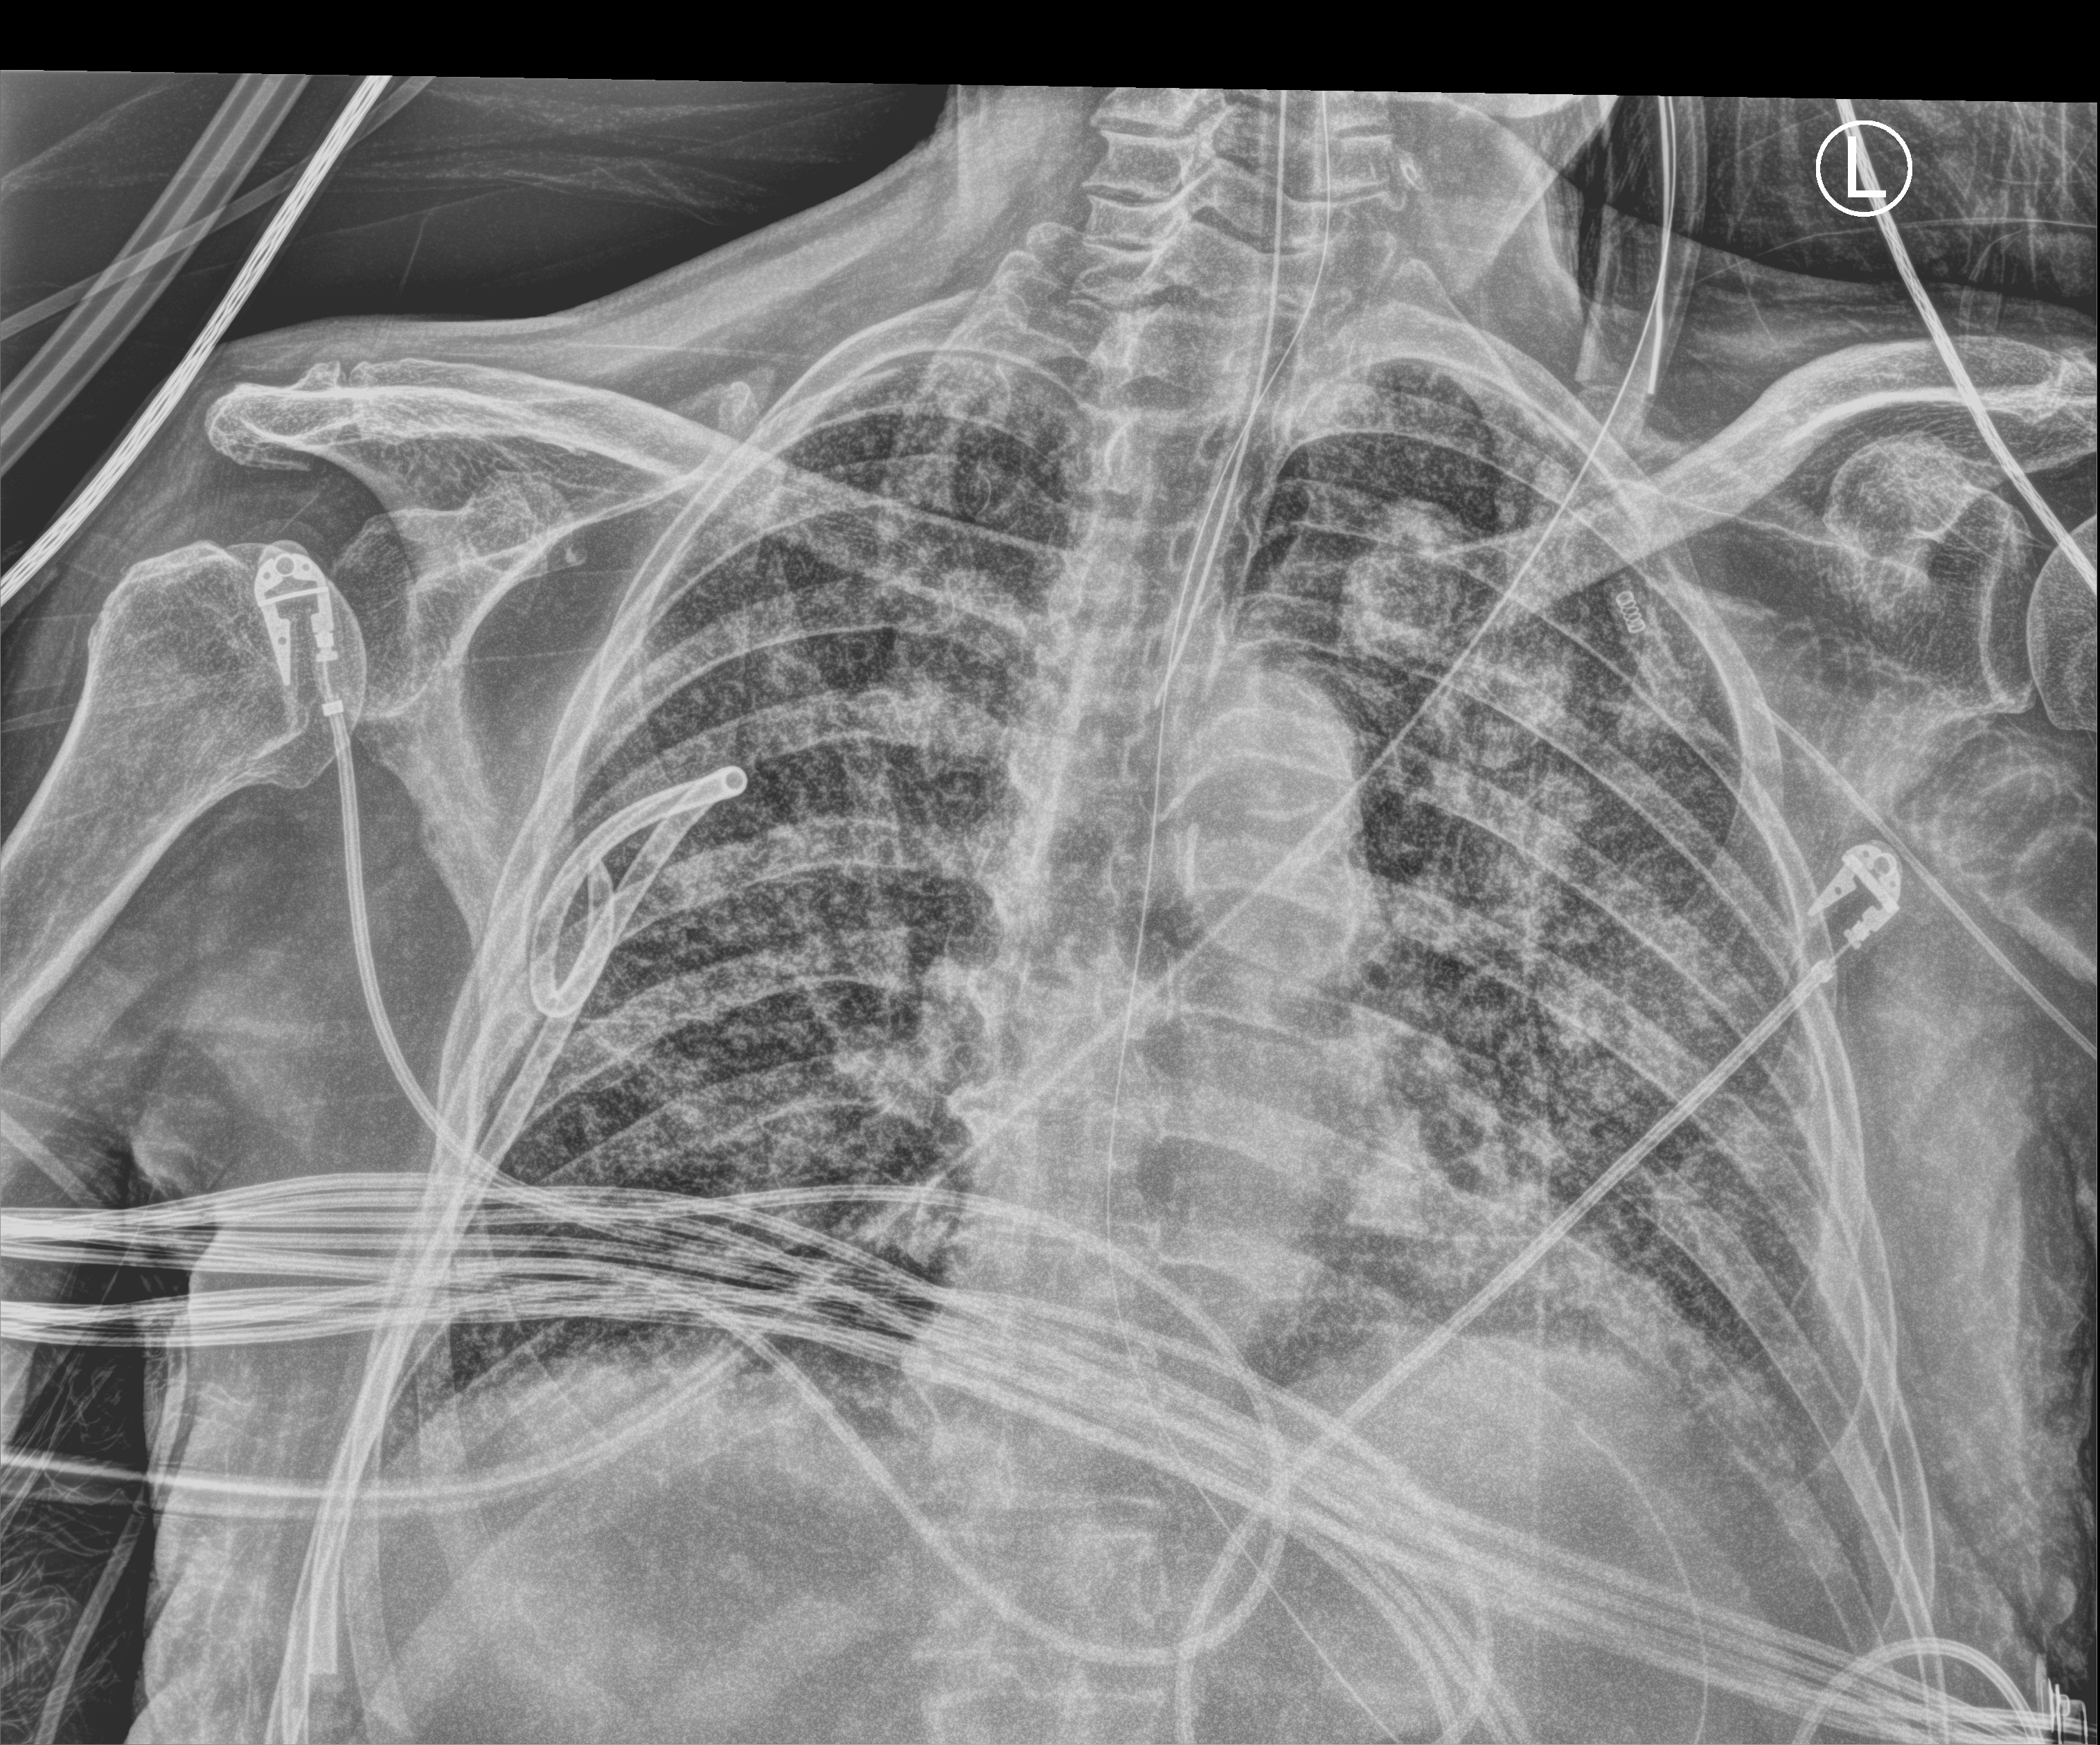
Portable chest radiograph; anteroposterior (AP) projection. Male patient hospitalised with COVID-19, age 75–90 years.
Admission-level facts for this patient (not findings on this image; timing relative to this image not recorded): mechanically ventilated during this hospital stay: yes.